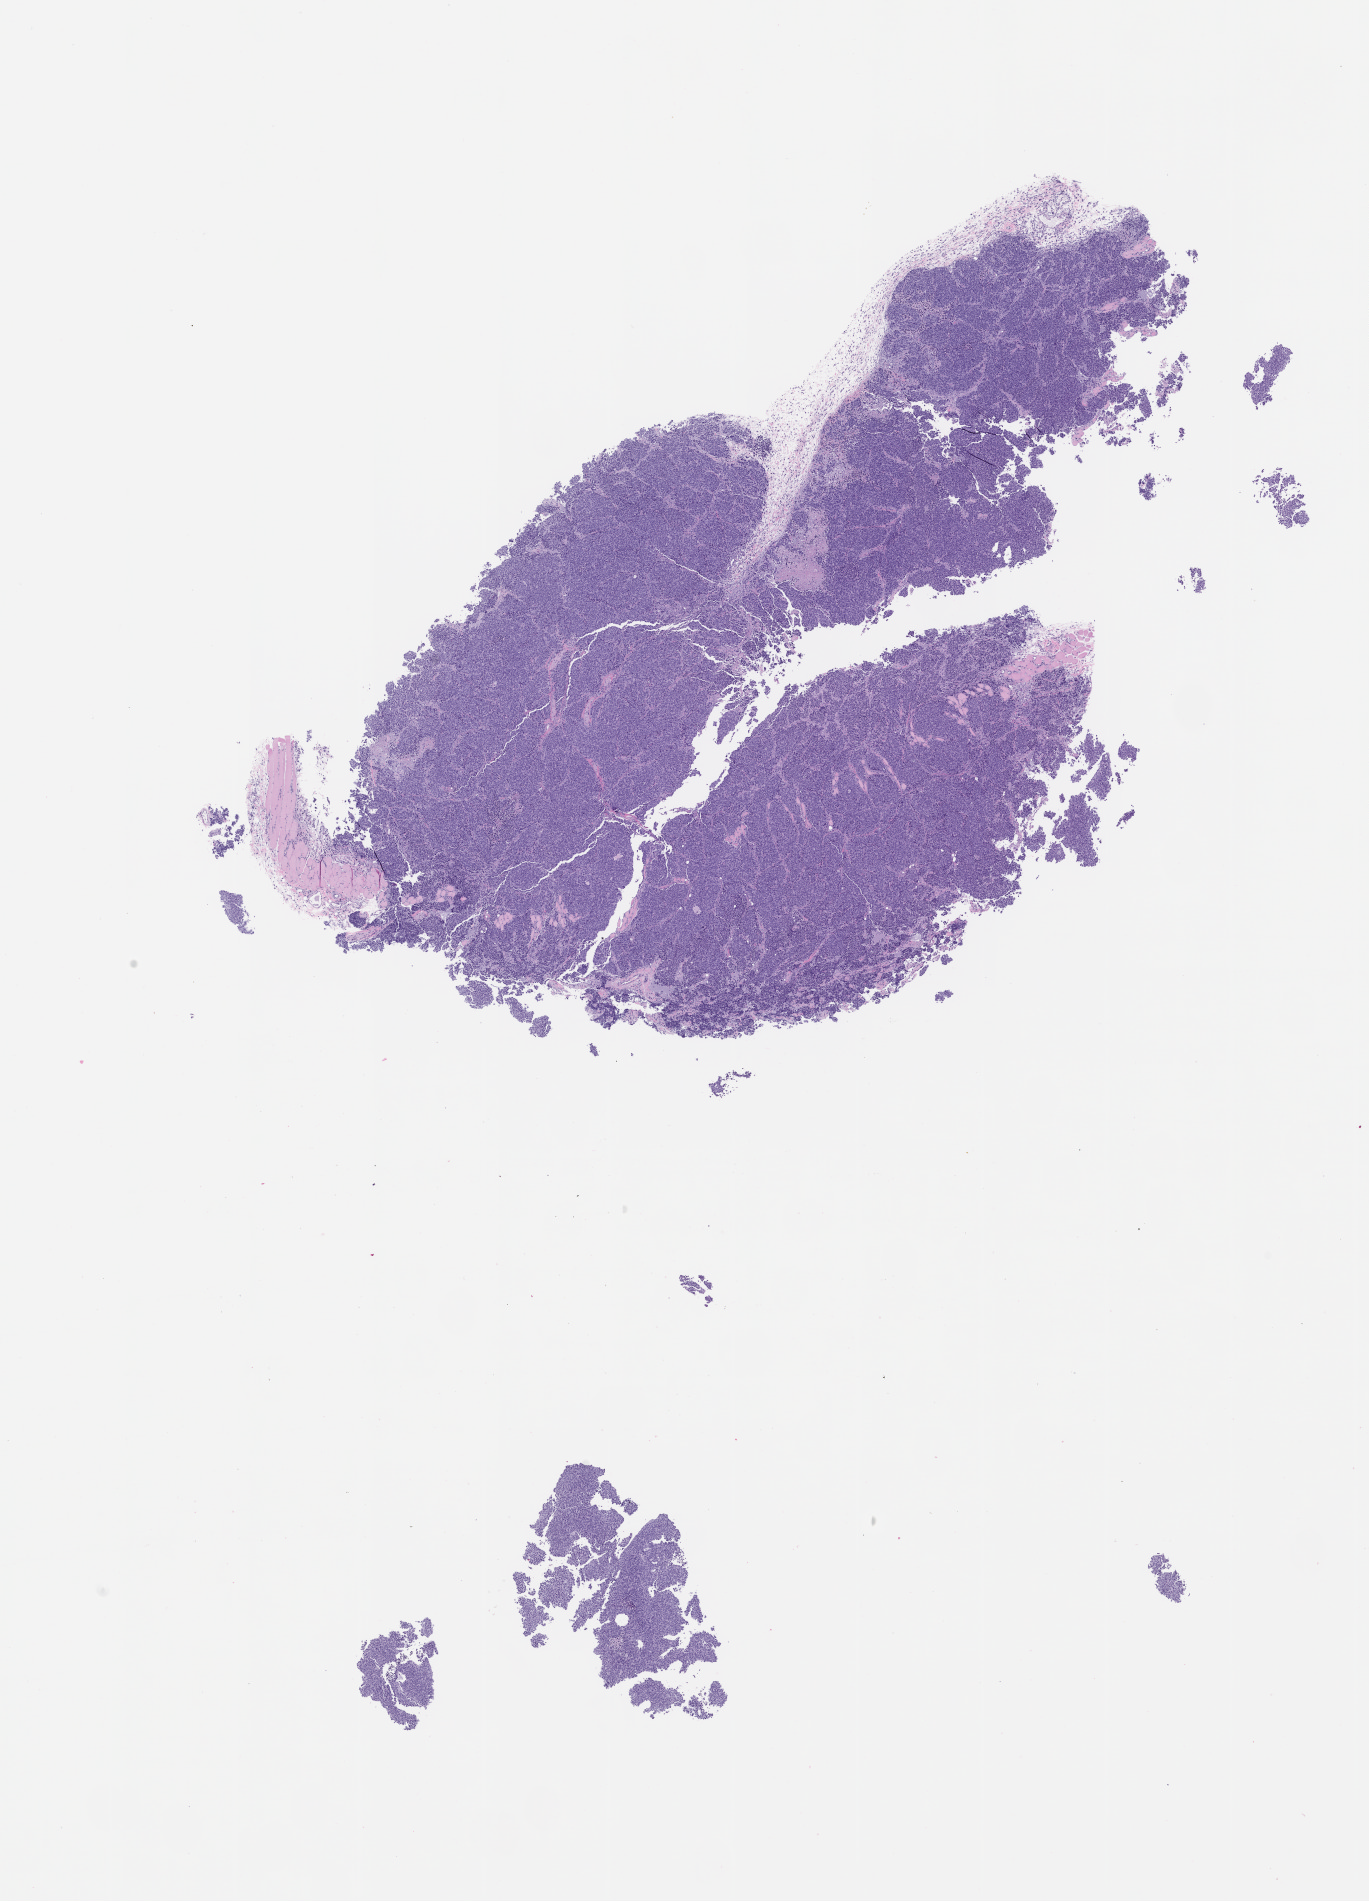
Whole-slide image, hematoxylin and eosin (H&E): patient-derived xenograft (human tumor grown in a mouse) — a low-resolution overview of the entire scanned area, about 11.0 x 15.2 mm. Formalin-fixed, paraffin-embedded (FFPE) tissue. Originating tumor site category: lung.
Originating patient diagnosis: Lung Adenocarcinoma.